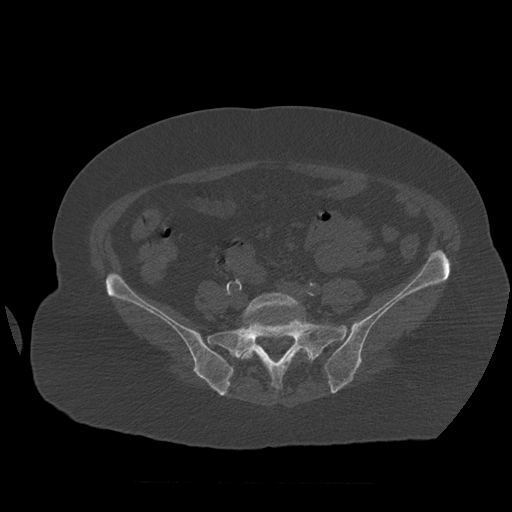
CT including the spine, one axial slice. Position 170 of 399 along the scan axis. Bone window (W 1800 / L 400 HU). 1.25 mm slice thickness. 512 × 512 image matrix, field of view 404 × 404 mm. Patient age 81 years. From the clinical record (not read from this slice): primary cancer: renal; vertebrae with lytic lesions (as recorded): L1.
Structures marked on this image (semi-automatically segmented with operator editing):
- L5 vertebra: bounding box [x1, y1, x2, y2] px = [242, 293, 311, 360]